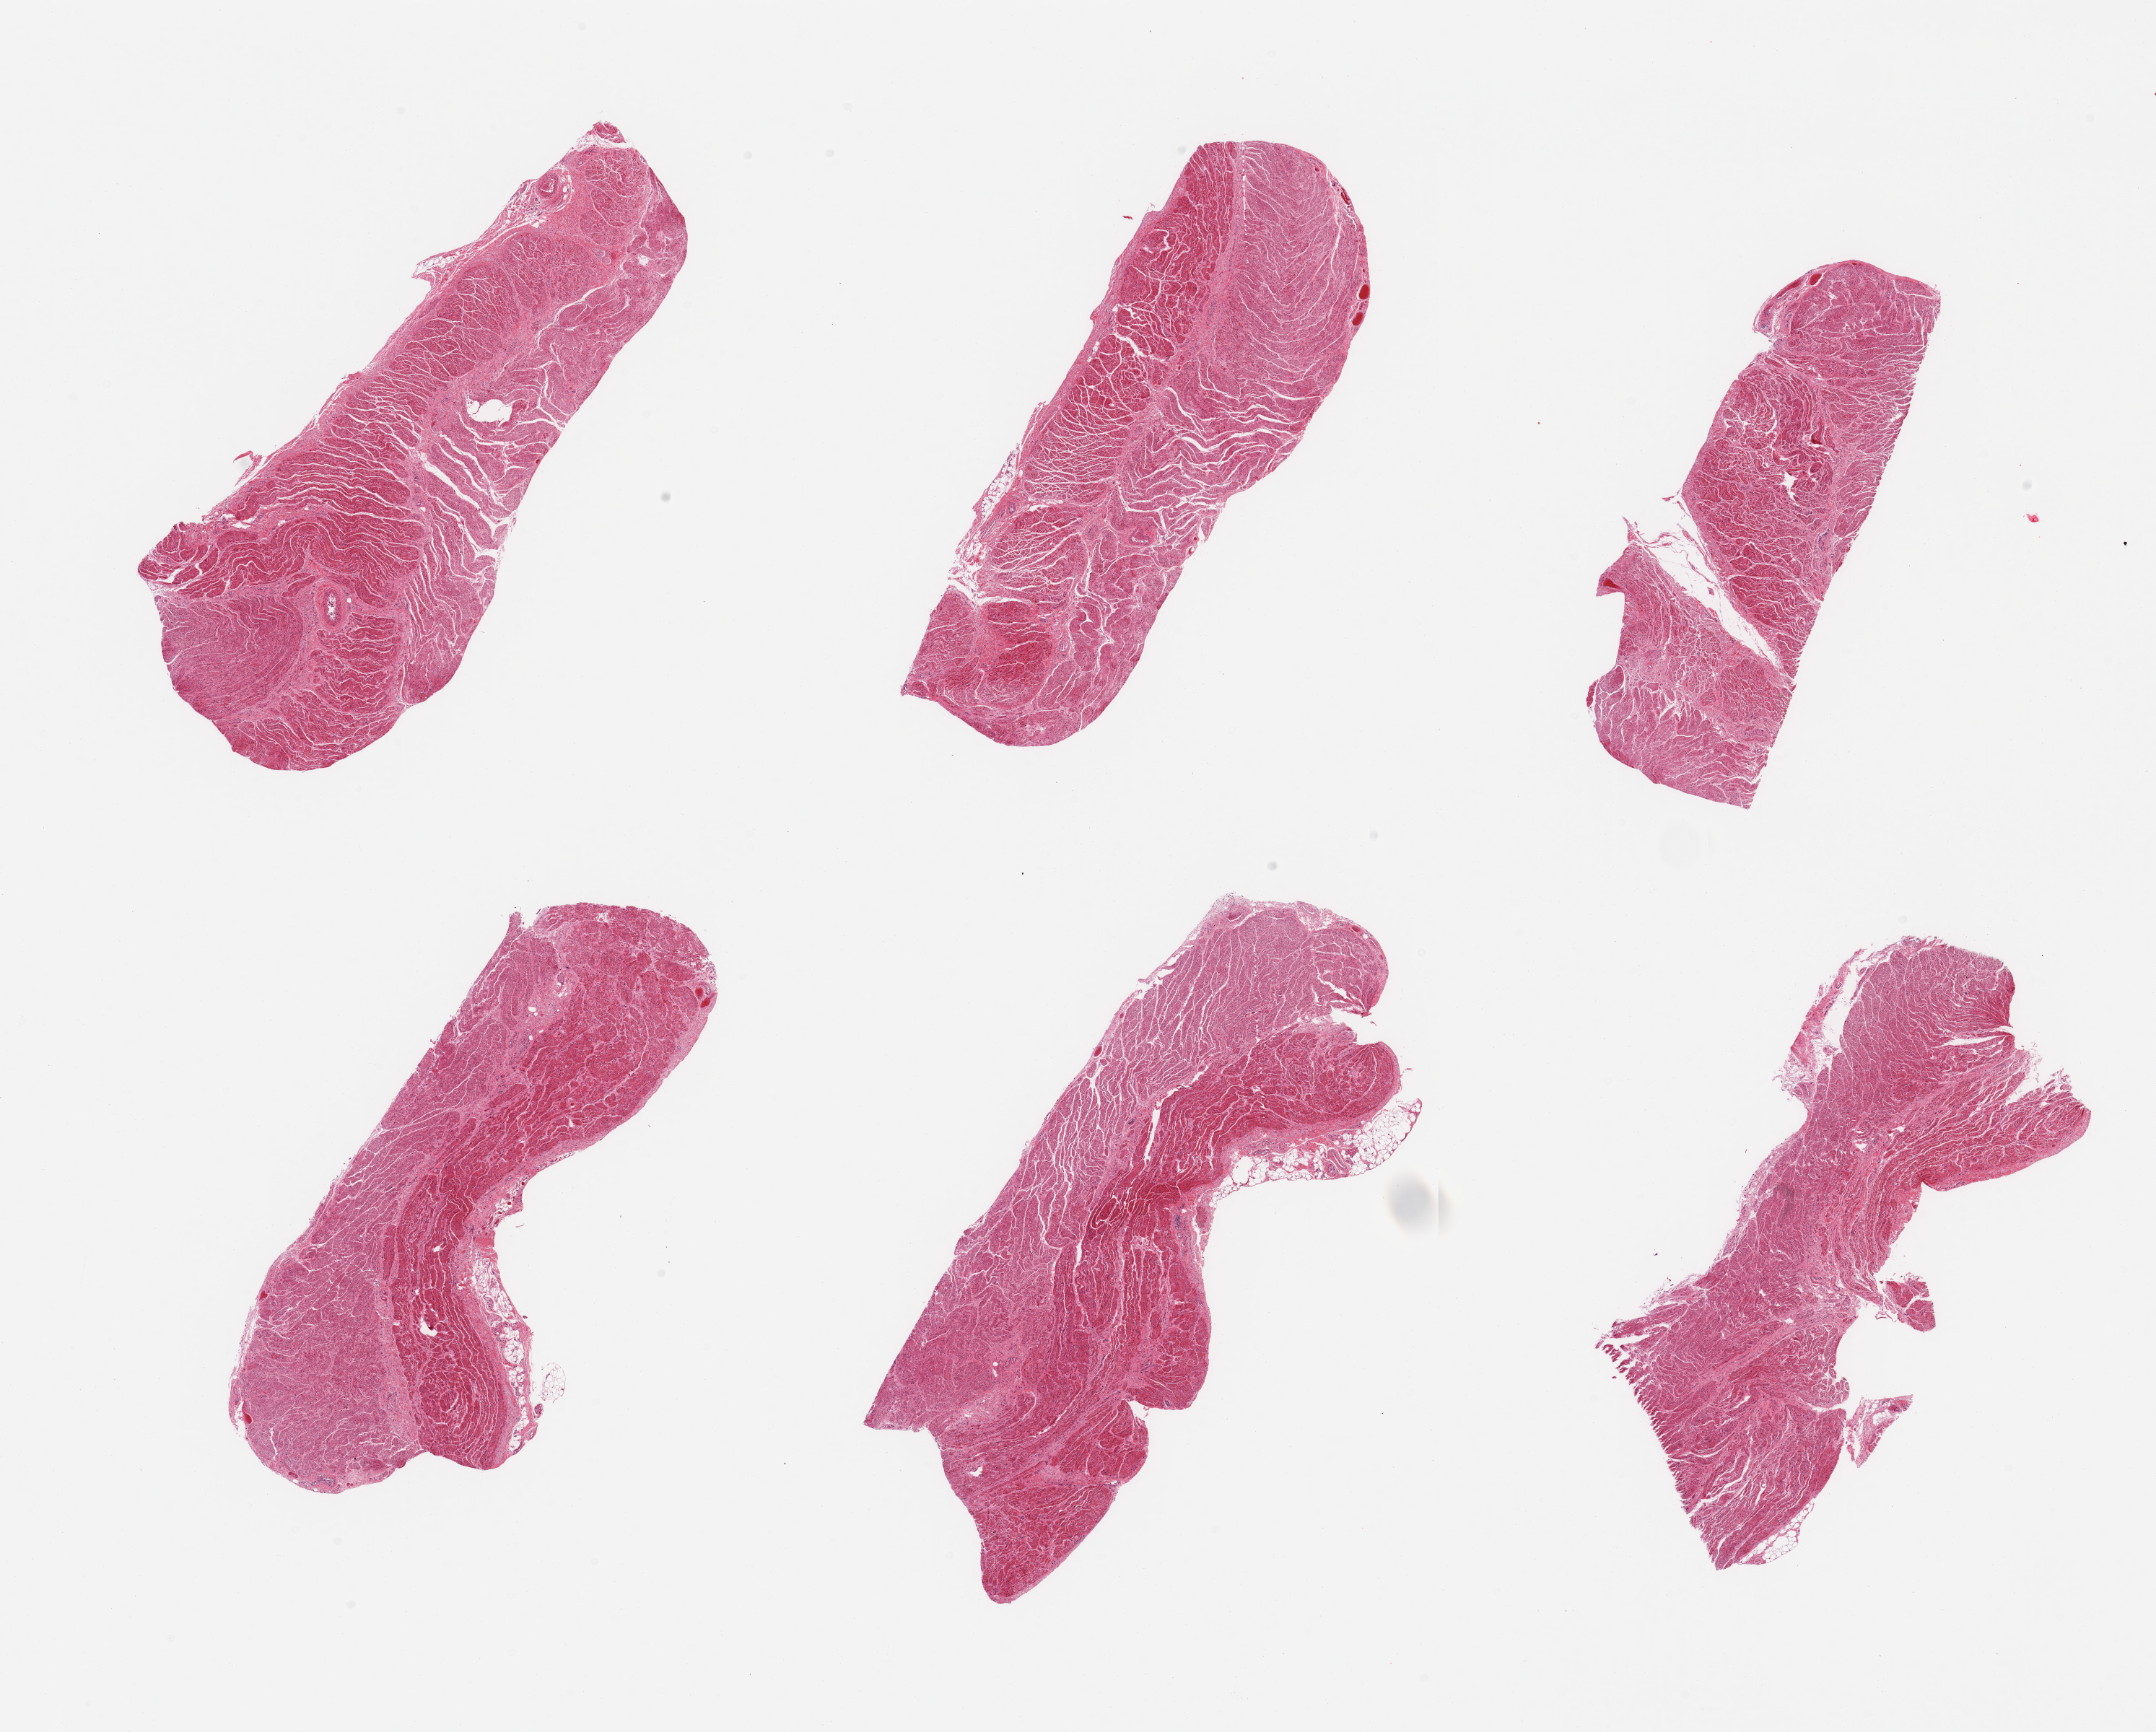
Whole-slide image, hematoxylin and eosin (H&E) stain, whole scanned area (about 23.6 x 19.0 mm) shown as a low-resolution overview. PAXgene-fixed, paraffin-embedded tissue. Section of gastroesophageal junction (target tissue). Tissue donor sample.
• reviewer comment on this tissue sample: 6 pieces, confirmed target muscularis